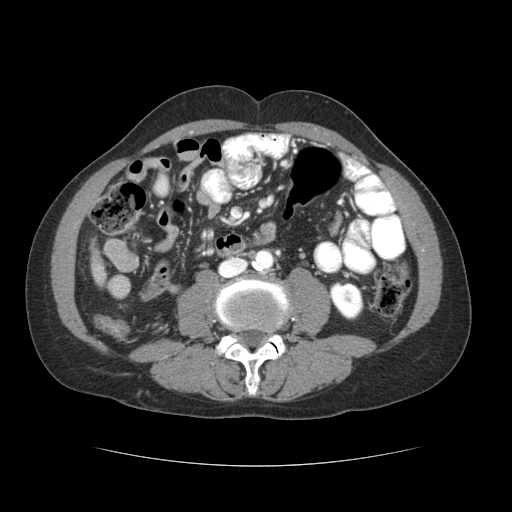
Contrast-enhanced abdominal CT (liver protocol), one axial slice. Position 4 of 69 along the scan axis. Reconstruction kernel STANDARD. Soft-tissue window (W 400 / L 40 HU). 2.5 mm slice thickness. 512 × 512 image matrix, field of view 360 × 360 mm. From the clinical record (not read from this slice): diagnosis: hepatocellular carcinoma (patient treated with transarterial chemoembolisation; whether this scan precedes or follows treatment is not stated here); TNM stage (as recorded): Stage-II; Child-Pugh class: B; tumour differentiation: poorly differentiated; tumour nodularity: multinodular.
Annotated regions visible in this slice (semi-automatic segmentation, software-assisted and operator-edited):
- liver parenchyma outside the tumour (the mass and vessels are separate outlines, so this box may not span the whole liver): bounding box <90,250,106,284> (left, top, right, bottom; pixels)
- liver vessels: <98,268,100,279>